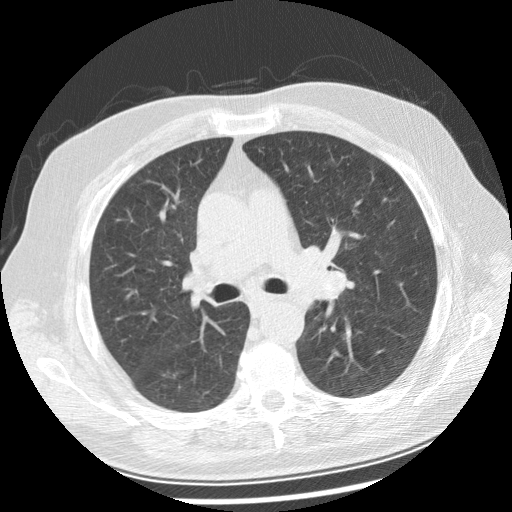
Chest CT (low-dose screening protocol), one axial image. Baseline screening round. Lung window (W 1500 / L -600 HU). 2.5 mm slice thickness. Standard (soft-tissue) reconstruction kernel (STANDARD). 512 × 512 image matrix. Male, age 70 years at enrolment.
• Lesion marked by an expert reader, bounding box (x1, y1, x2, y2) in pixels: (279, 242, 360, 305).
• No non-calcified nodule or mass ≥4 mm was recorded by the screening reader at this exam.
• Lung cancer was diagnosed 29 days after this screen: squamous cell carcinoma, keratinizing, NOS, left main stem bronchus, moderately differentiated (G2), stage IIIB (AJCC 6th edition), 40 mm at pathology.